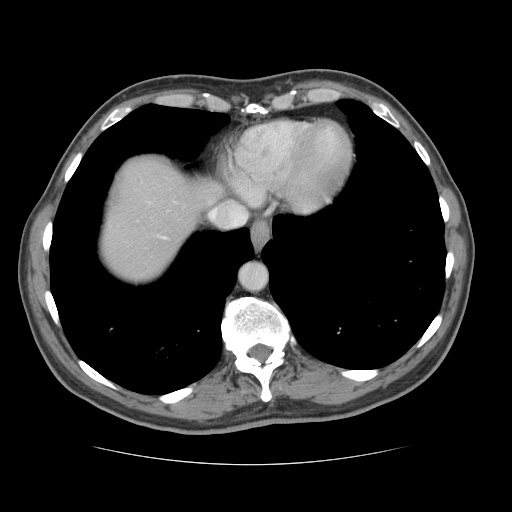
Contrast-enhanced abdominal CT, one axial slice; slice 118 of 134 in the series (ordered by position); soft-tissue window (W 400 / L 40 HU); 2.5 mm slice thickness; 512 × 512 image matrix, field of view 377 × 377 mm. Male patient, age 68 years. Case-level facts recorded for this patient, not image findings: diagnosis: colorectal cancer liver metastases, imaged before liver resection; multiple liver metastases: yes; largest metastasis: 2.2 cm; disease in both lobes: no.
Annotated regions visible in this slice (manually delineated by an expert):
- hepatic veins: box from (x=227, y=204) to (x=245, y=214) px
- liver: (x=102, y=161)–(x=214, y=282)
- planned liver remnant (the part of the liver to remain after resection): (x=102, y=161)–(x=214, y=282)